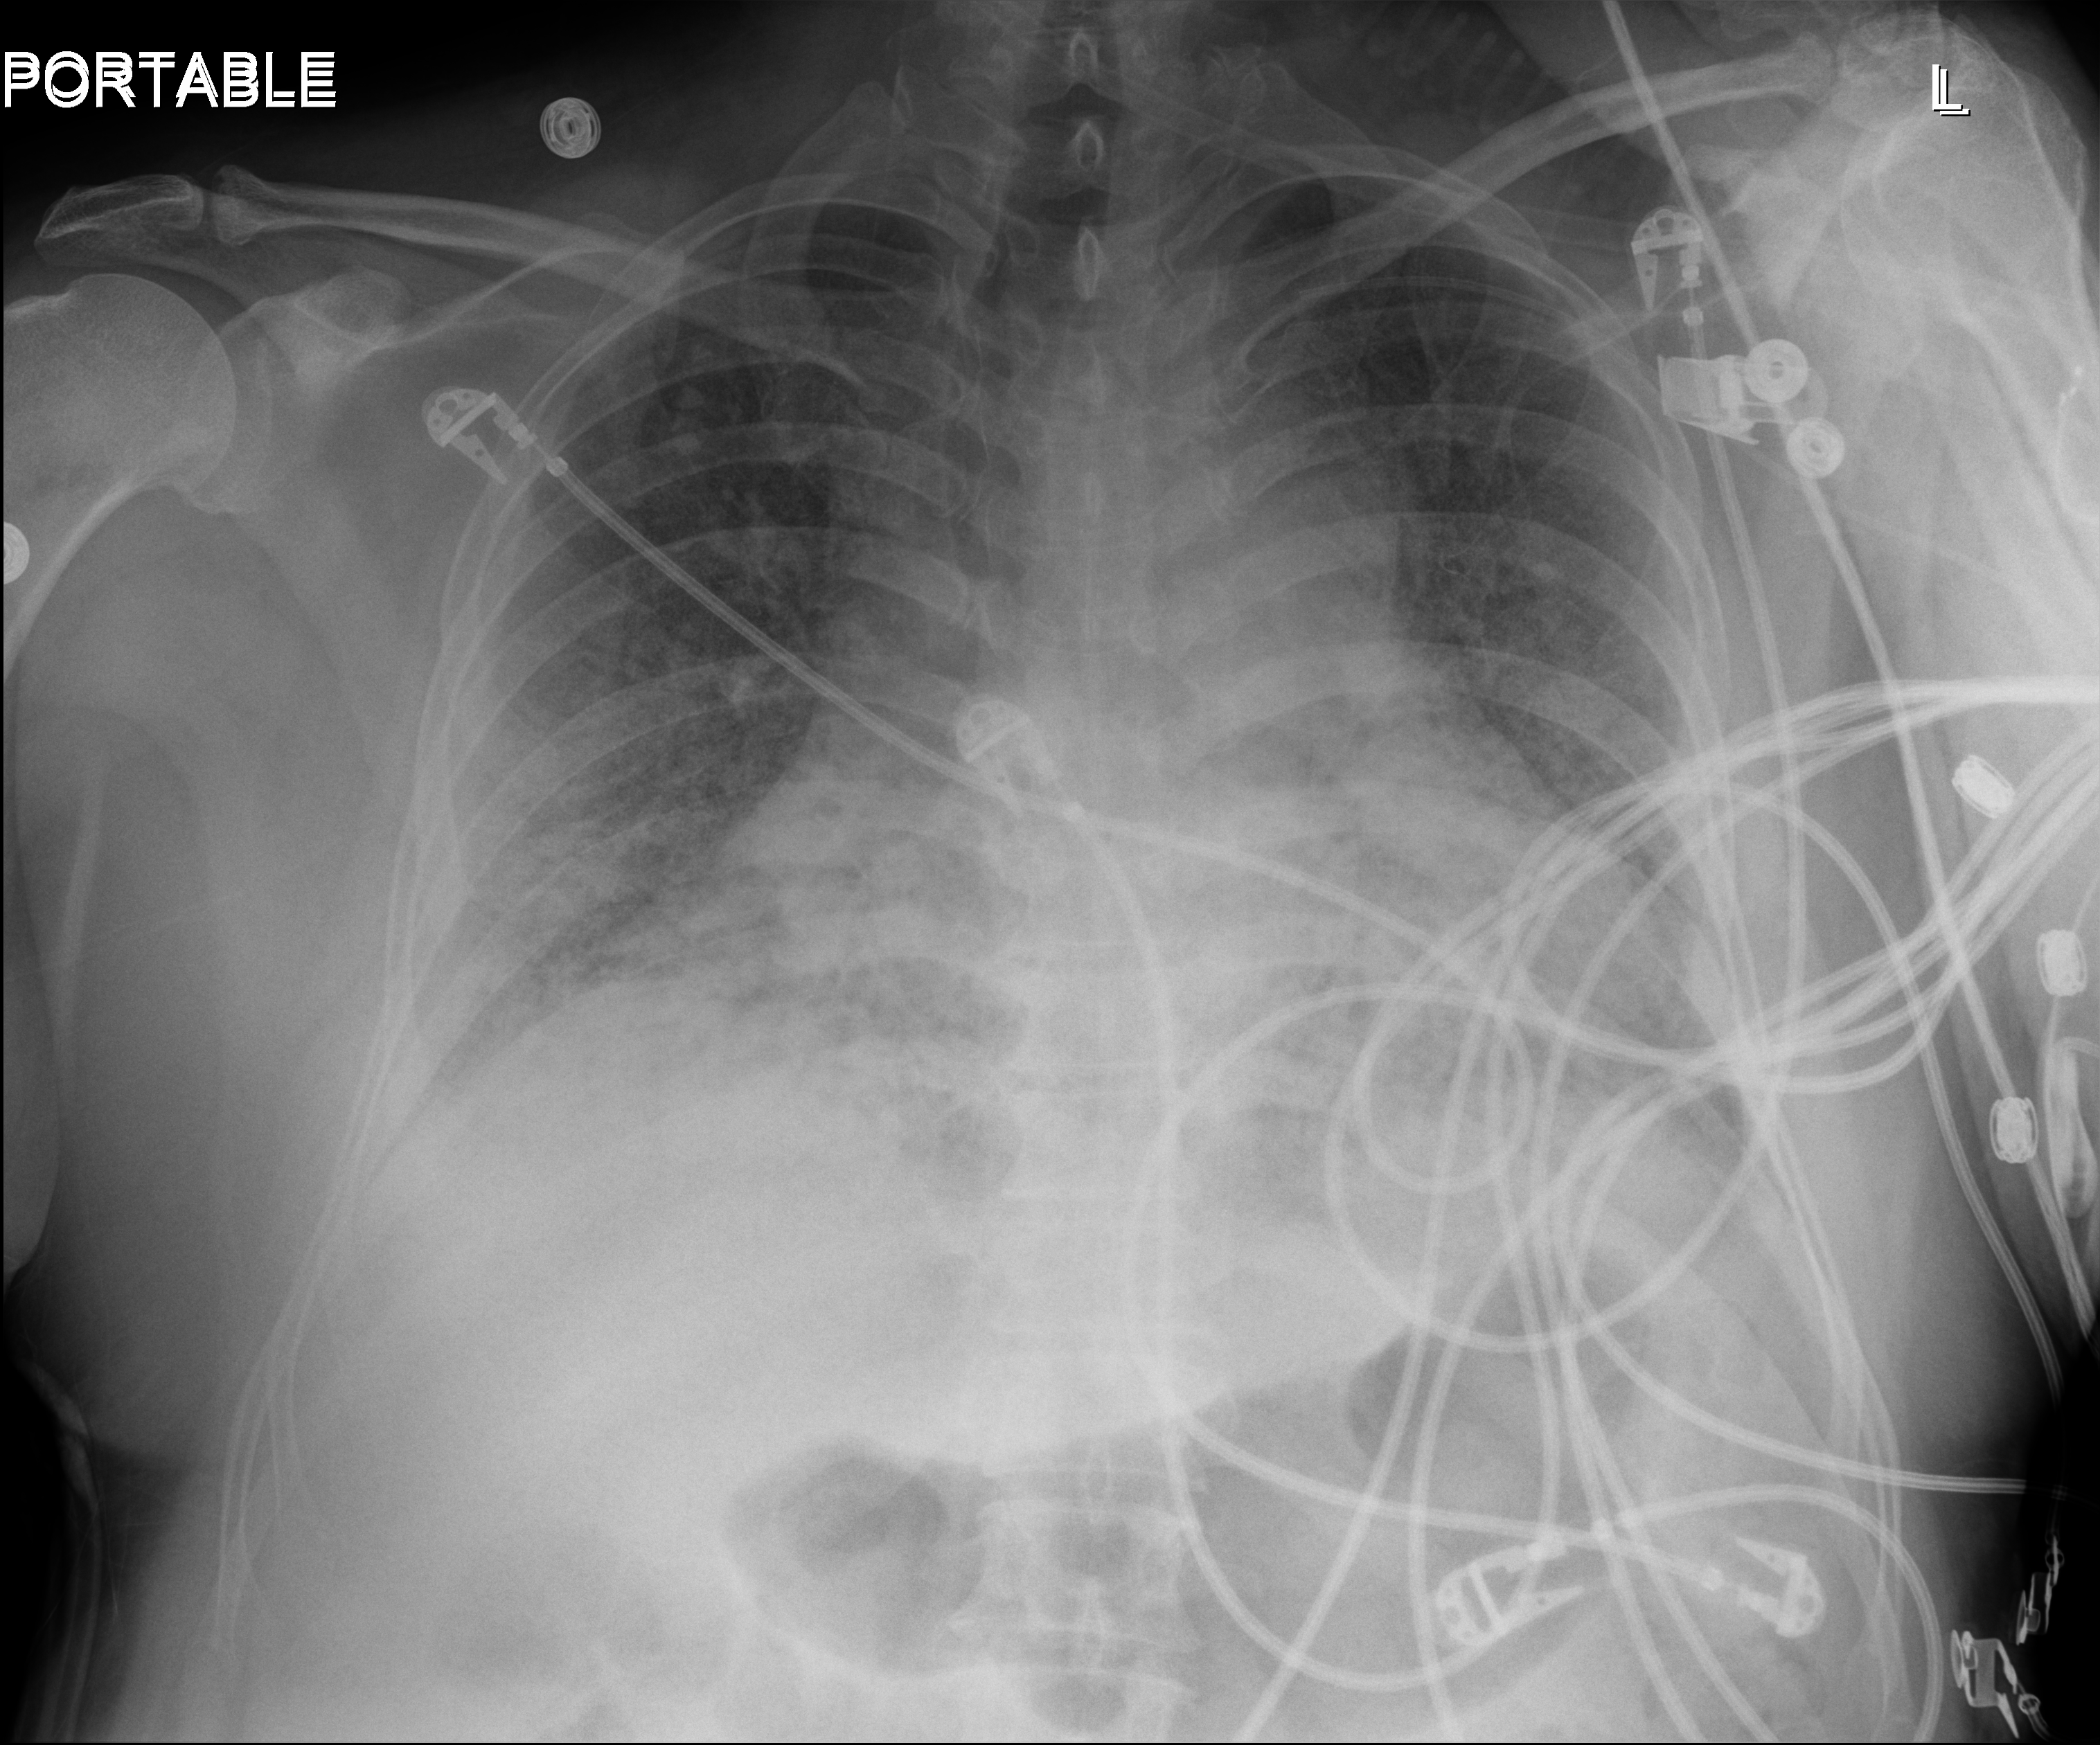
Chest X-ray (portable). Adult patient hospitalised with COVID-19, age 18–59 years.
From the hospital-stay record, not from the radiograph (when in the stay this image was taken is not recorded):
- other chronic lung disease (admission record): no